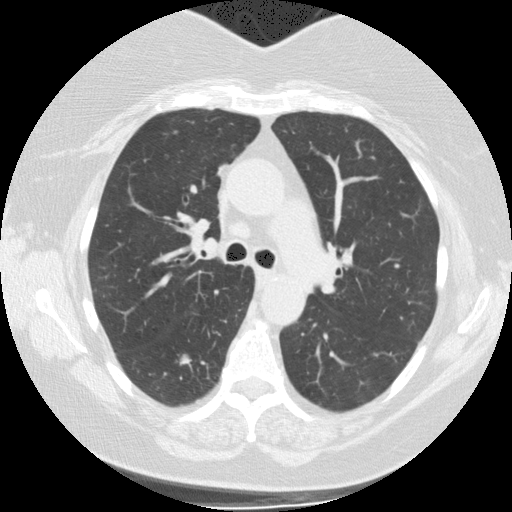
Low-dose screening chest CT, axial slice. Baseline annual screen. Lung window (W 1500 / L -600 HU). Slice 45 of 130 in the series. 512 × 512 image matrix. Female, age 62 years at enrolment. Current smoker at enrolment.
- Lesion marked by an expert reader, bounding box <199,153,240,191> (left, top, right, bottom; pixels).
- The screening reader recorded 3 non-calcified nodules or masses ≥4 mm on this exam (right lower lobe, right lower lobe, right lower lobe); which of them this box marks is not recorded.
- Official screen result: positive, change unspecified: nodule(s) >= 4 mm or enlarging nodule(s), mass(es), or other non-specific abnormalities suspicious for lung cancer.
- Participant outcome: lung cancer diagnosed 929 days after this screen — adenocarcinoma, NOS, right upper lobe, poorly differentiated (G3), stage IB (AJCC 6th edition), 12 mm at pathology.